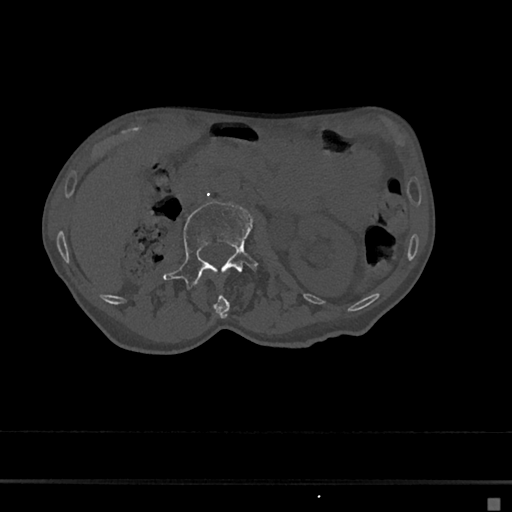
CT including the spine, one axial slice; position 20 of 797 along the scan axis; reconstruction kernel Br40s/3; 120 kVp; bone window (W 1800 / L 400 HU); 512 × 512 image matrix. Female patient, age 68 years. Case-level facts recorded for this patient, not image findings: primary cancer: renal.
Annotated regions visible in this slice (semi-automatically segmented with operator editing):
- L1 vertebra: bounding box <198,282,229,319> (left, top, right, bottom; pixels)
- L2 vertebra: <163,201,262,291>